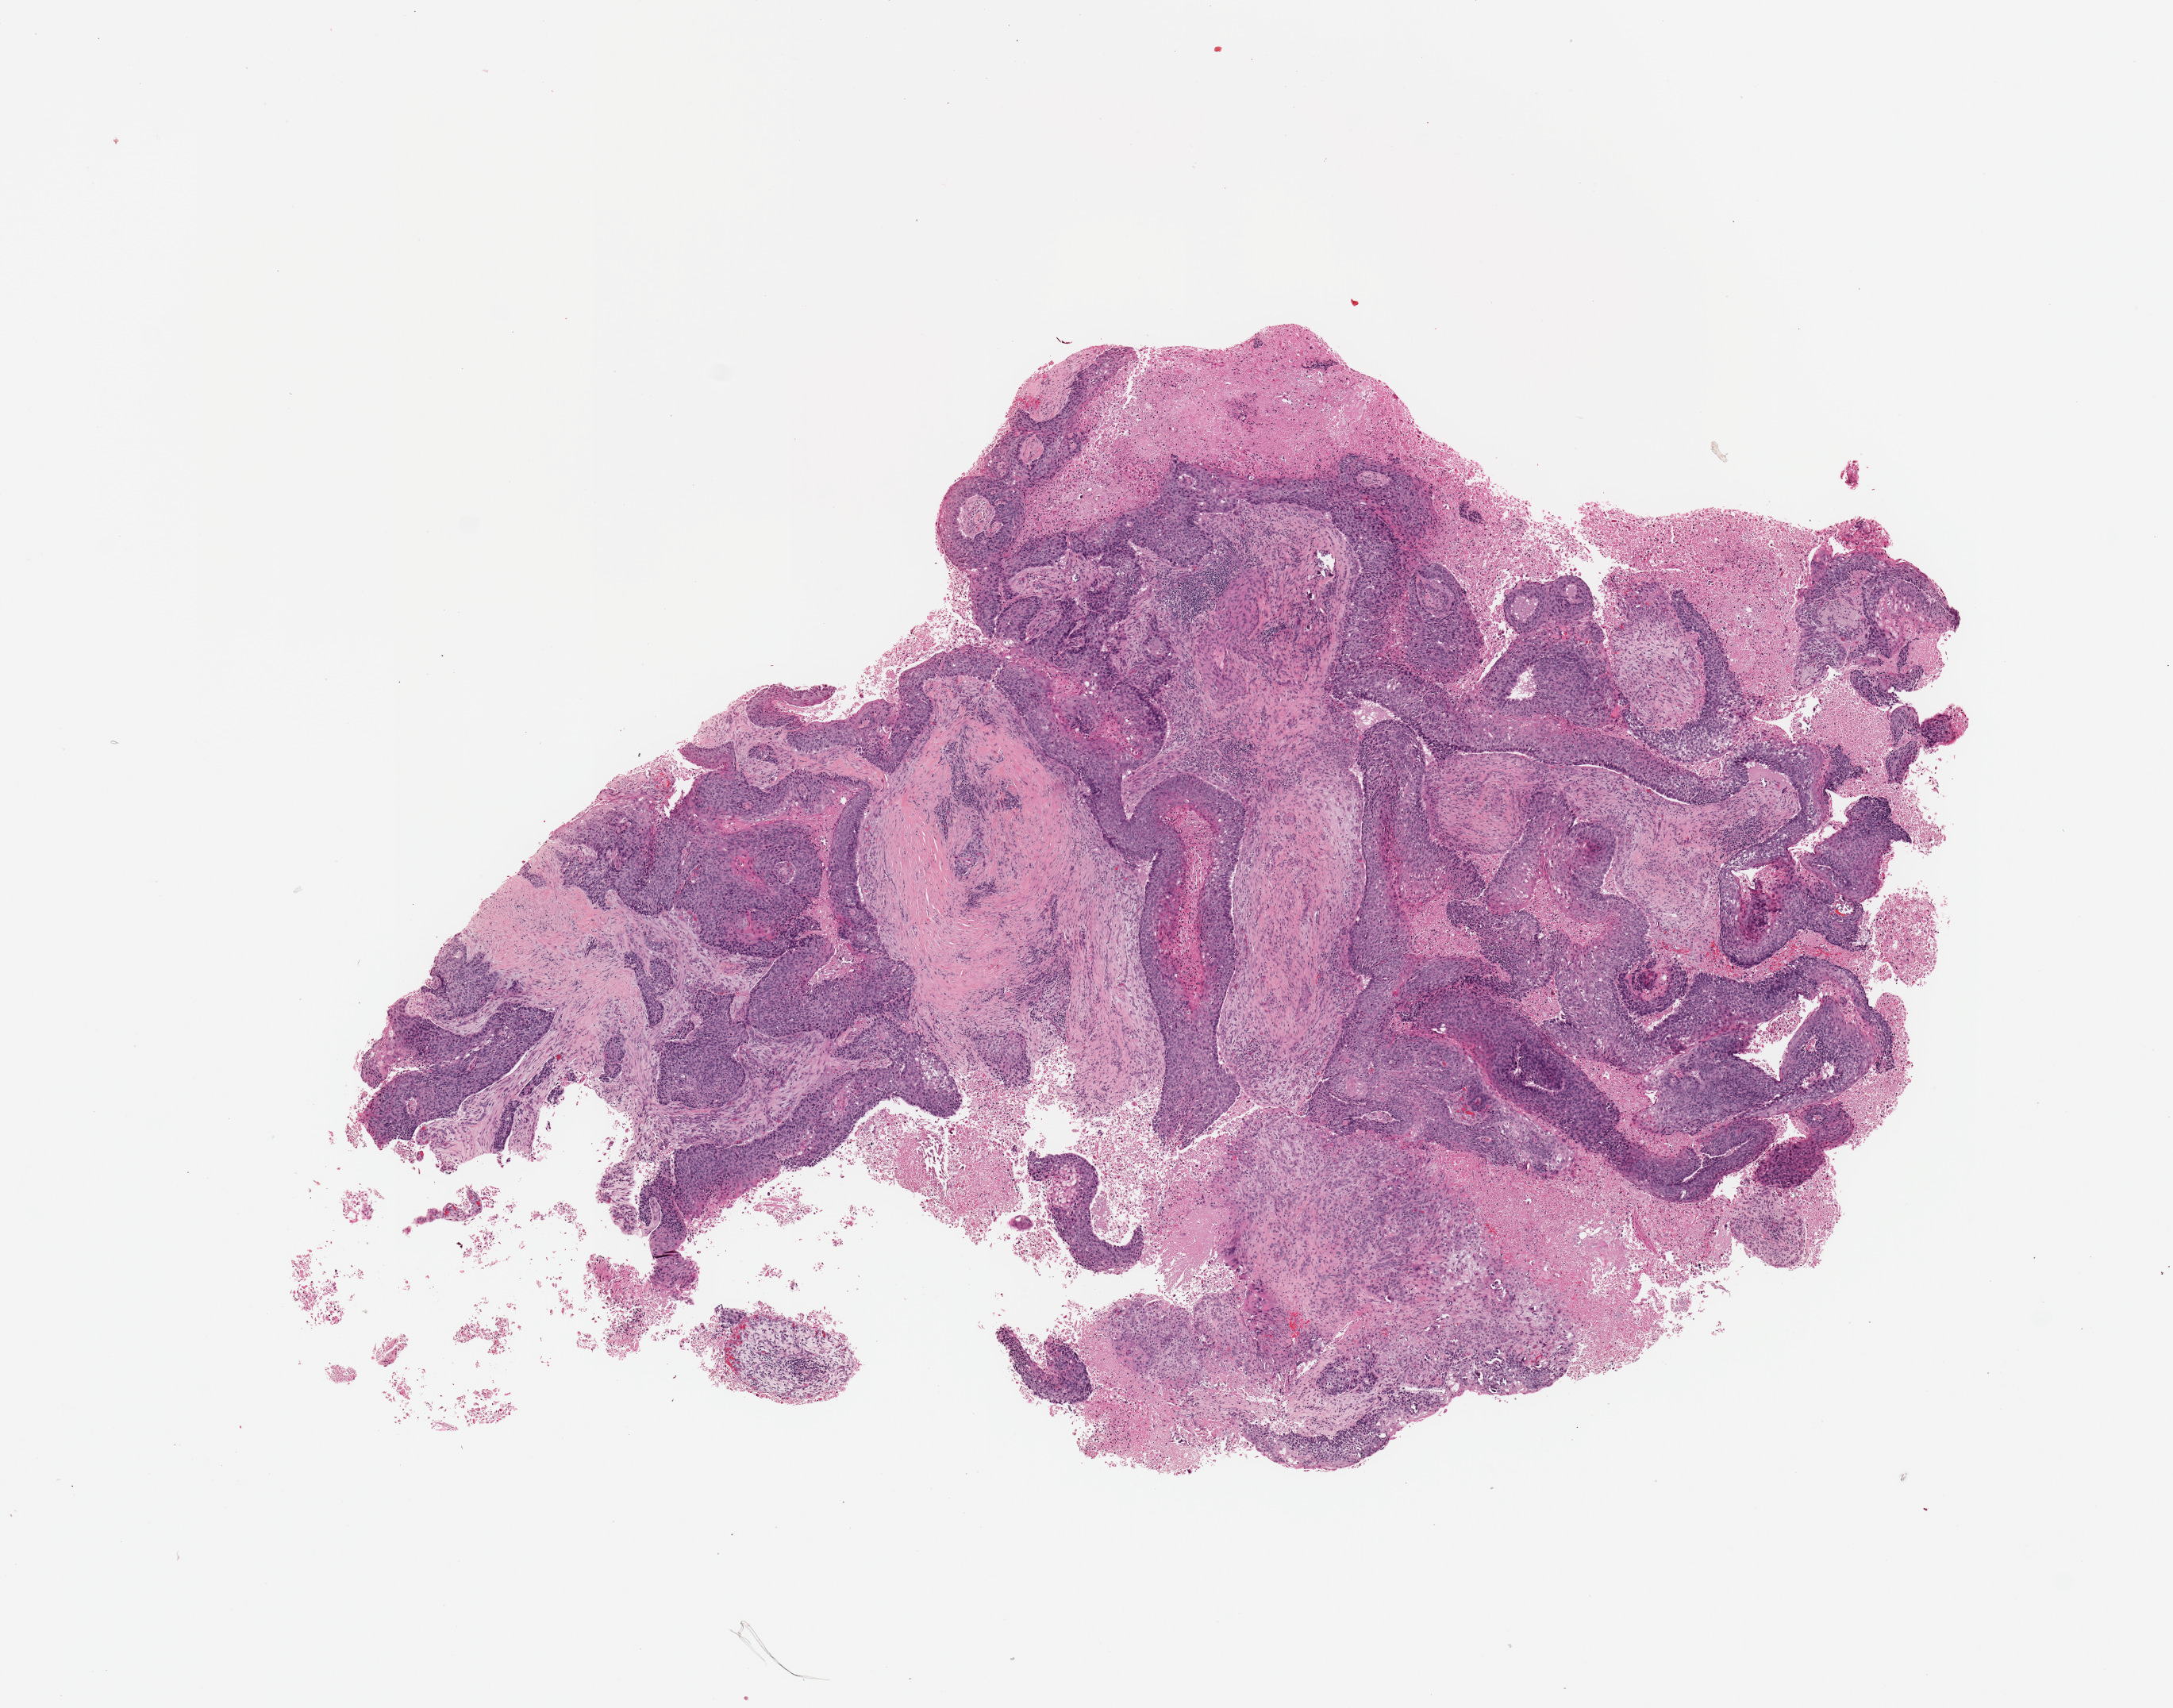
Whole-slide histology image, H&E-stained, low-resolution overview of the scanned area, about 10.8 x 8.5 mm (slide scanned at 20x); lung, tumour tissue. Patient: male, age 78 years. Histologic grade: G2 (moderately differentiated).
* primary tumour site (as recorded): right middle lobe
* AJCC pathologic stage: III
* histologic diagnosis: Squamous cell carcinoma, NOS